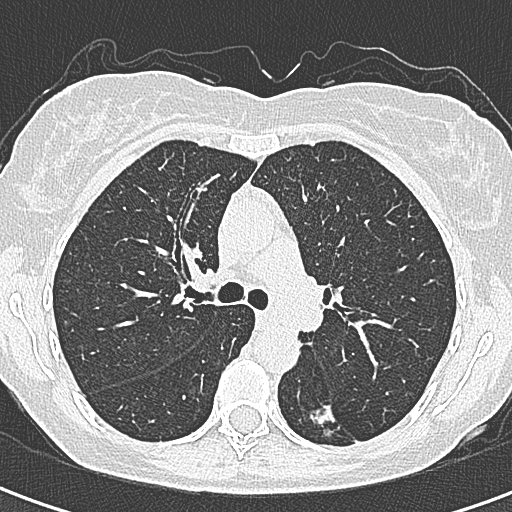
Low-dose screening chest CT, axial slice. First (baseline) screen. Lung window (W 1500 / L -600 HU). Lung (sharp) reconstruction kernel (B80f). 120 kVp. 512 × 512 image matrix. Female participant, aged 58 years at enrolment. Former smoker at enrolment.
- Expert reader's lesion annotation, bounding box [x1, y1, x2, y2] px = [290, 391, 361, 454].
- The screening reader recorded 2 non-calcified nodules or masses ≥4 mm on this exam (left lower lobe, right lower lobe); which of them this box marks is not recorded.
- Official screen result: positive, change unspecified: nodule(s) >= 4 mm or enlarging nodule(s), mass(es), or other non-specific abnormalities suspicious for lung cancer.
- Lung cancer was diagnosed 22 days after this screen: adenocarcinoma, NOS, left lower lobe, moderately differentiated (G2), stage IA (AJCC 6th edition), 25 mm at pathology.